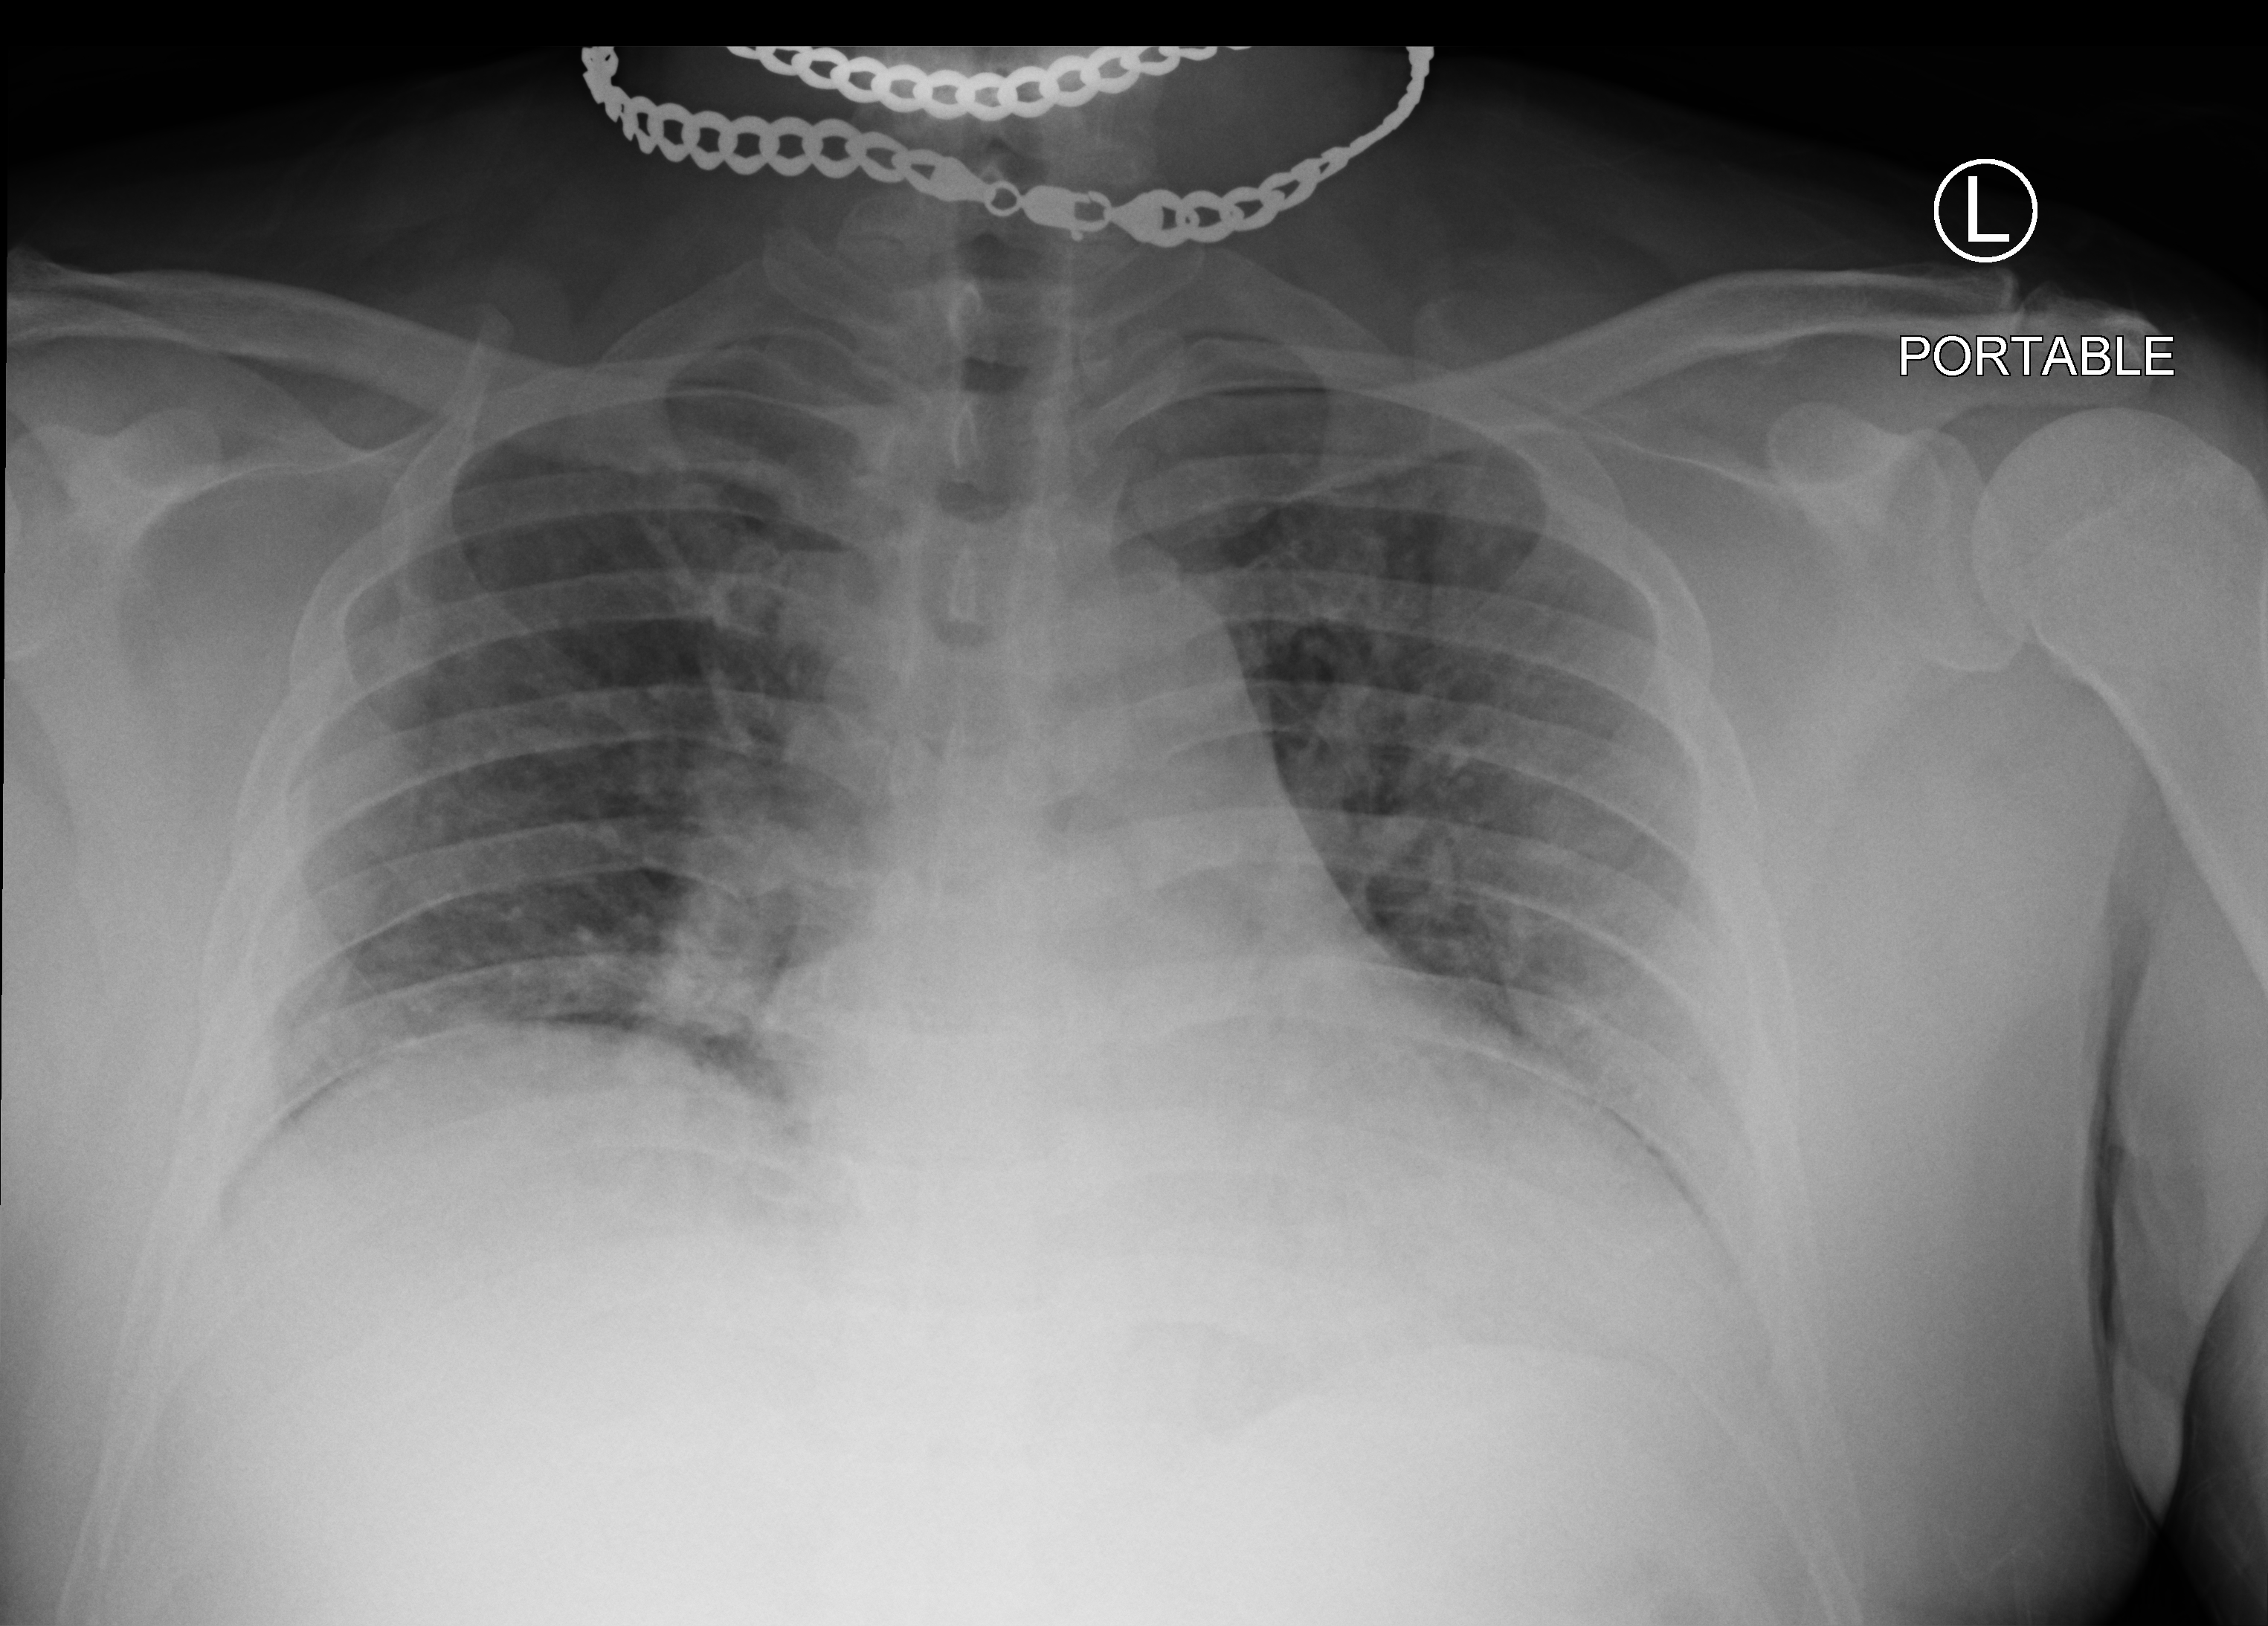
Bedside chest radiograph (computed radiography), anteroposterior (AP) projection. Male patient hospitalised with COVID-19, age 18–59 years.
Admission-level facts for this patient (not findings on this image; timing relative to this image not recorded): mechanically ventilated during this hospital stay: no.